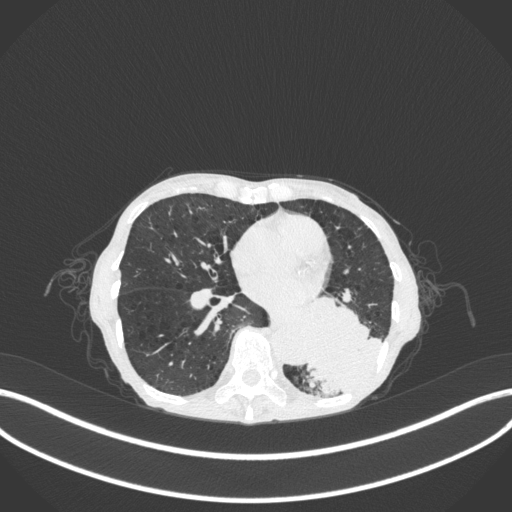
Chest CT, one axial slice; position 118 of 347 along the scan axis; reconstruction kernel B31f; lung window (W 1500 / L -600 HU); 1 mm slice thickness; 512 × 512 image matrix. Female patient, age 70 years. From the clinical record (not read from this slice): clinical TNM (as recorded): T3 N0 M0.
Outlined on this slice (rectangle marked by the reading radiologist):
- lung tumour (recorded histology: small cell carcinoma): bounding box [x1, y1, x2, y2] px = [295, 289, 387, 395]